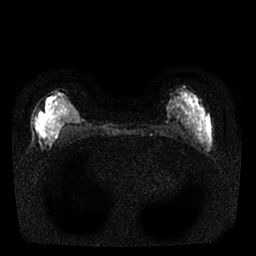
Breast MRI, one axial slice. Position 7 of 25 along the scan axis. Diffusion-weighted series; image 2 of 4 stored at this slice position (different b-values; order by instance number). 1.5 T. 256 × 256 image matrix, field of view 310 × 310 mm. Female patient.
Outlined on this slice (outlined manually by an expert reader):
- tumour on diffusion-weighted imaging: bounding box [x1, y1, x2, y2] px = [37, 119, 46, 137]